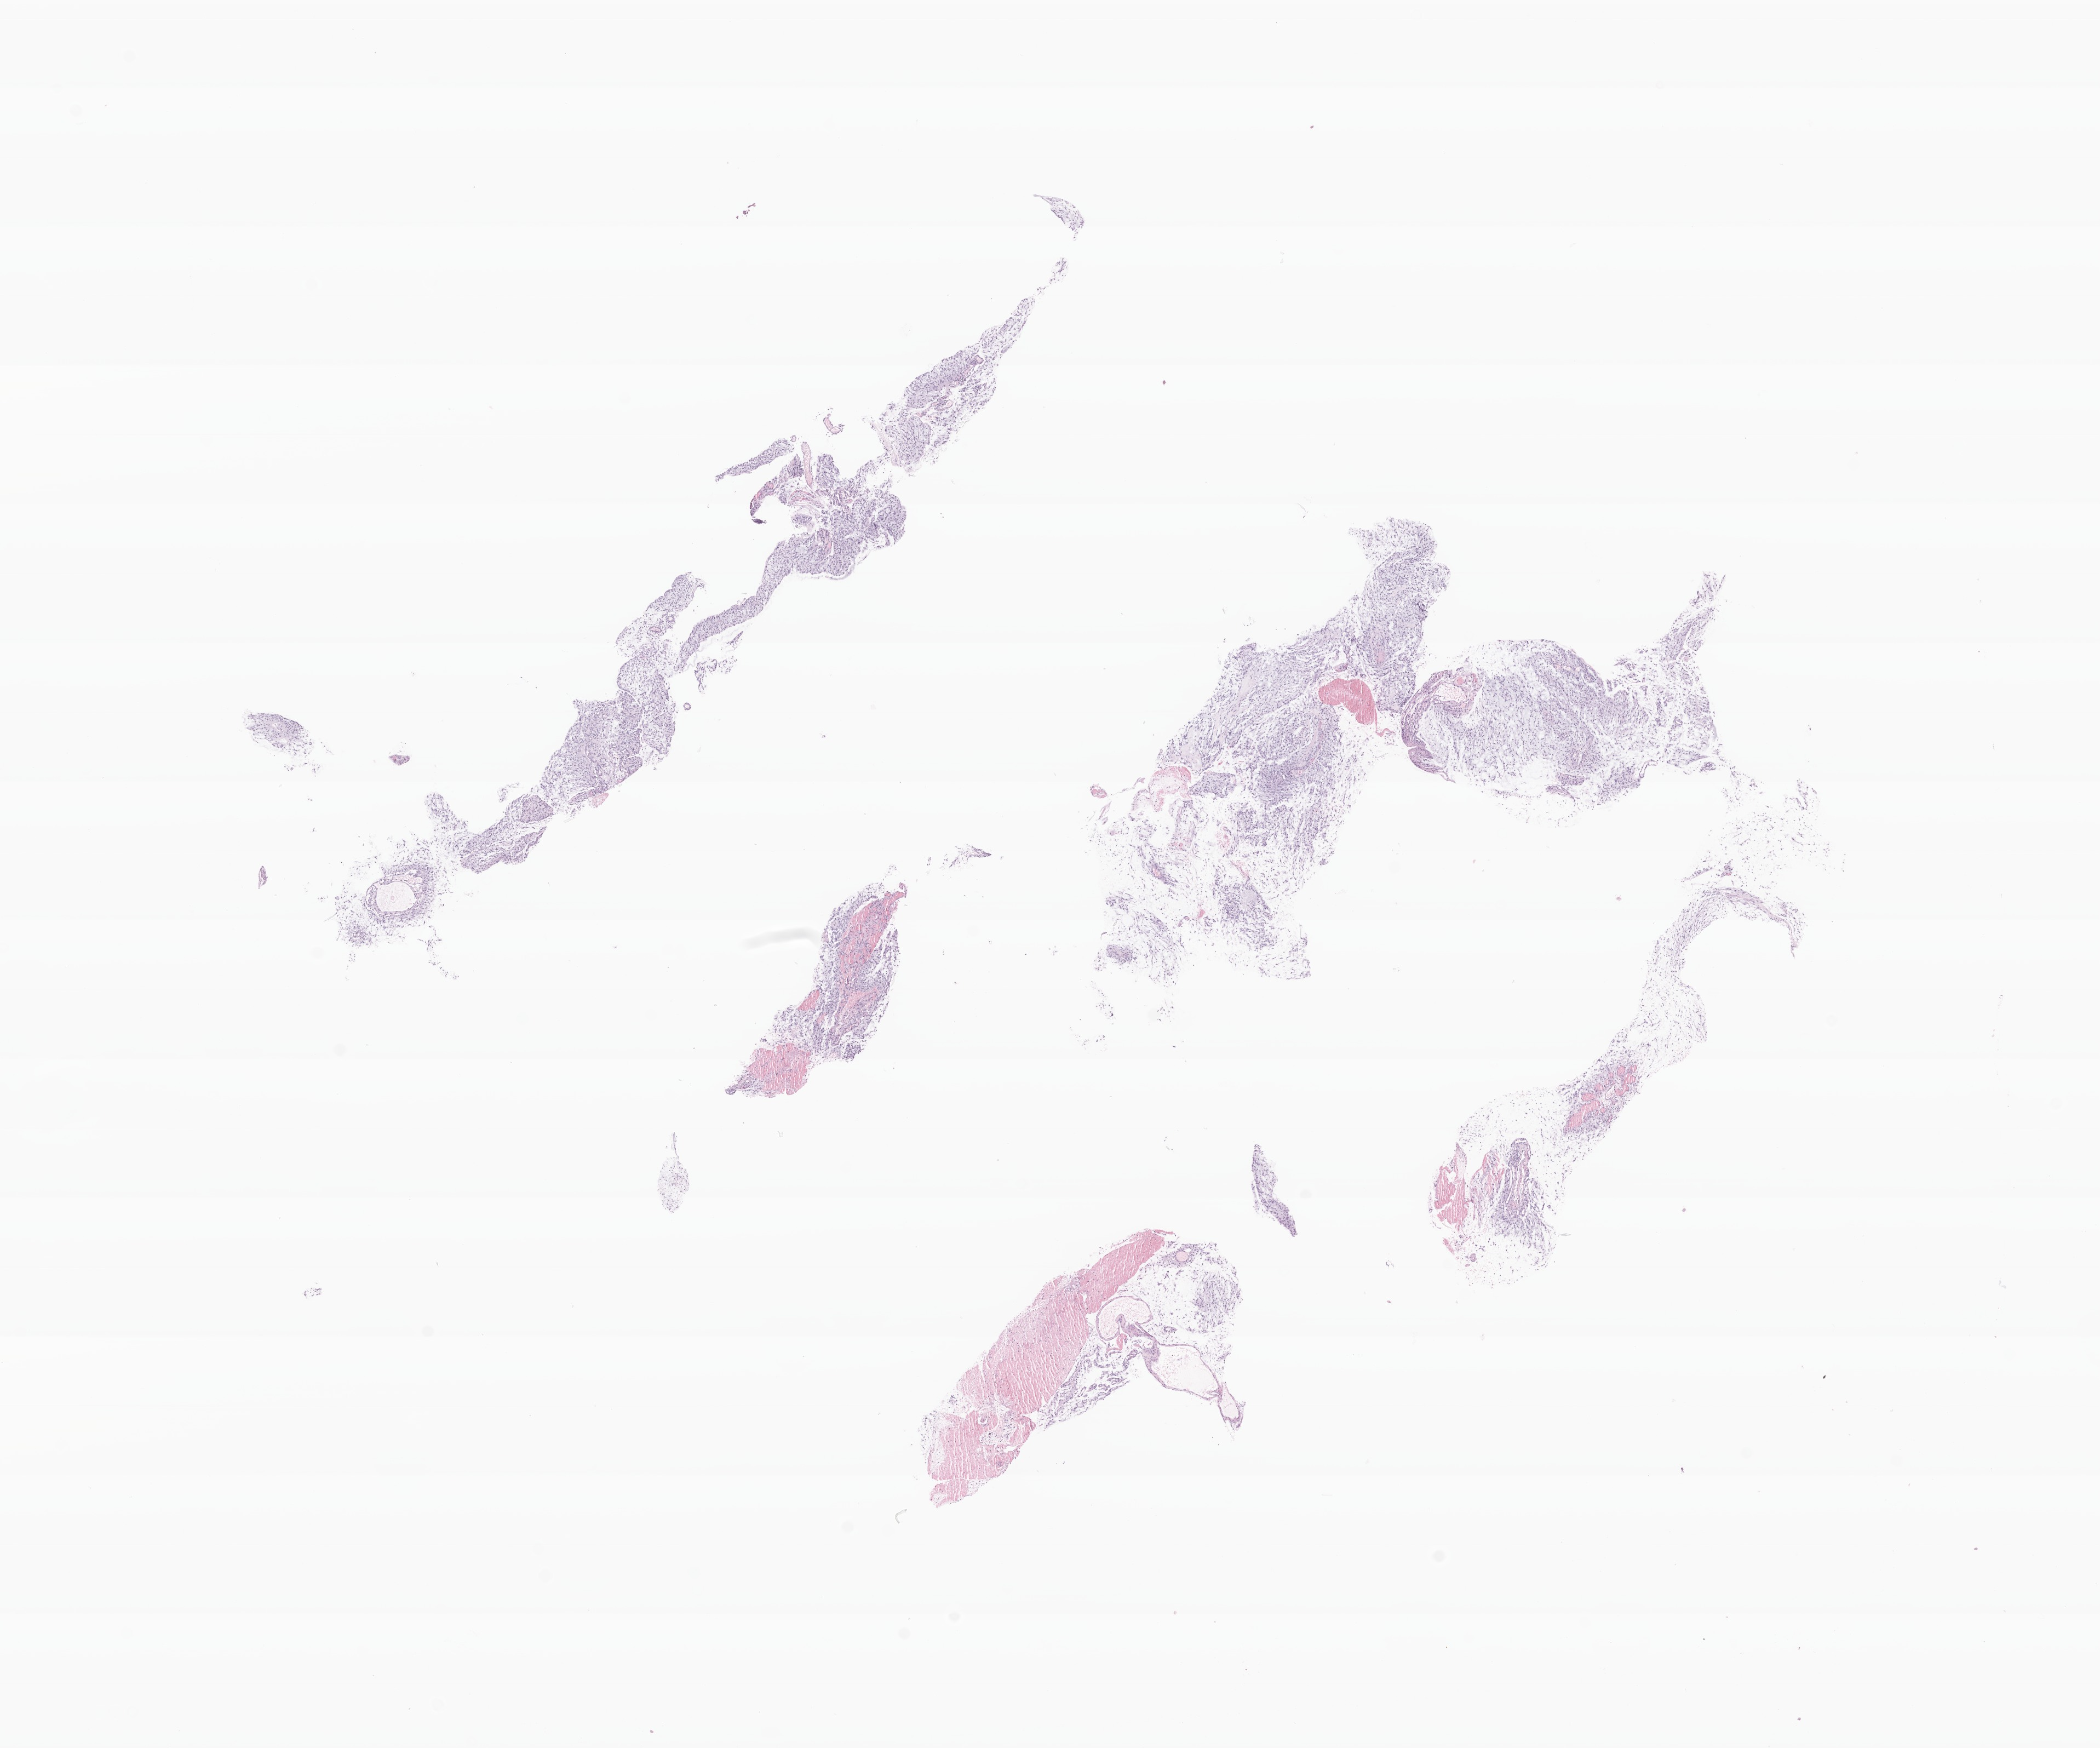
Hematoxylin and eosin (H&E) whole-slide image of tumor tissue from the brain — shown as a low-resolution overview of the whole scanned area (about 16.1 x 13.4 mm). Formalin-fixed paraffin-embedded section. Patient: male, age 63 months (5 years 3 months).
* recorded diagnosis: Pilocytic astrocytoma